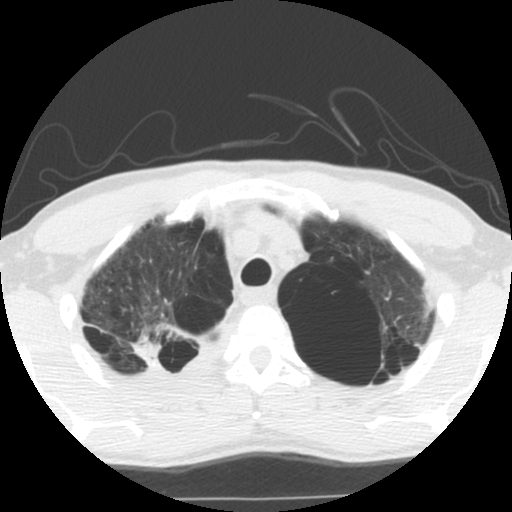
Low-dose screening chest CT, axial slice, second screening round (one year after baseline), lung window (W 1500 / L -600 HU), 2.5 mm slice thickness, standard (soft-tissue) reconstruction kernel (STANDARD). Male participant, aged 62 years at enrolment. Current smoker at enrolment.
- Expert reader's lesion annotation, bounding box <119,315,206,385> (left, top, right, bottom; pixels).
- The exam's reader record, not a measurement of the box and not confirmed to be the same lesion: non-calcified nodule or mass ≥4 mm, 35 × 25 mm, soft tissue attenuation.
- Official screen result: positive, other.
- Lung cancer was diagnosed 14 days after this screen: non-small cell carcinoma, right upper lobe, poorly differentiated (G3), stage IA (AJCC 6th edition), 70 mm at pathology.